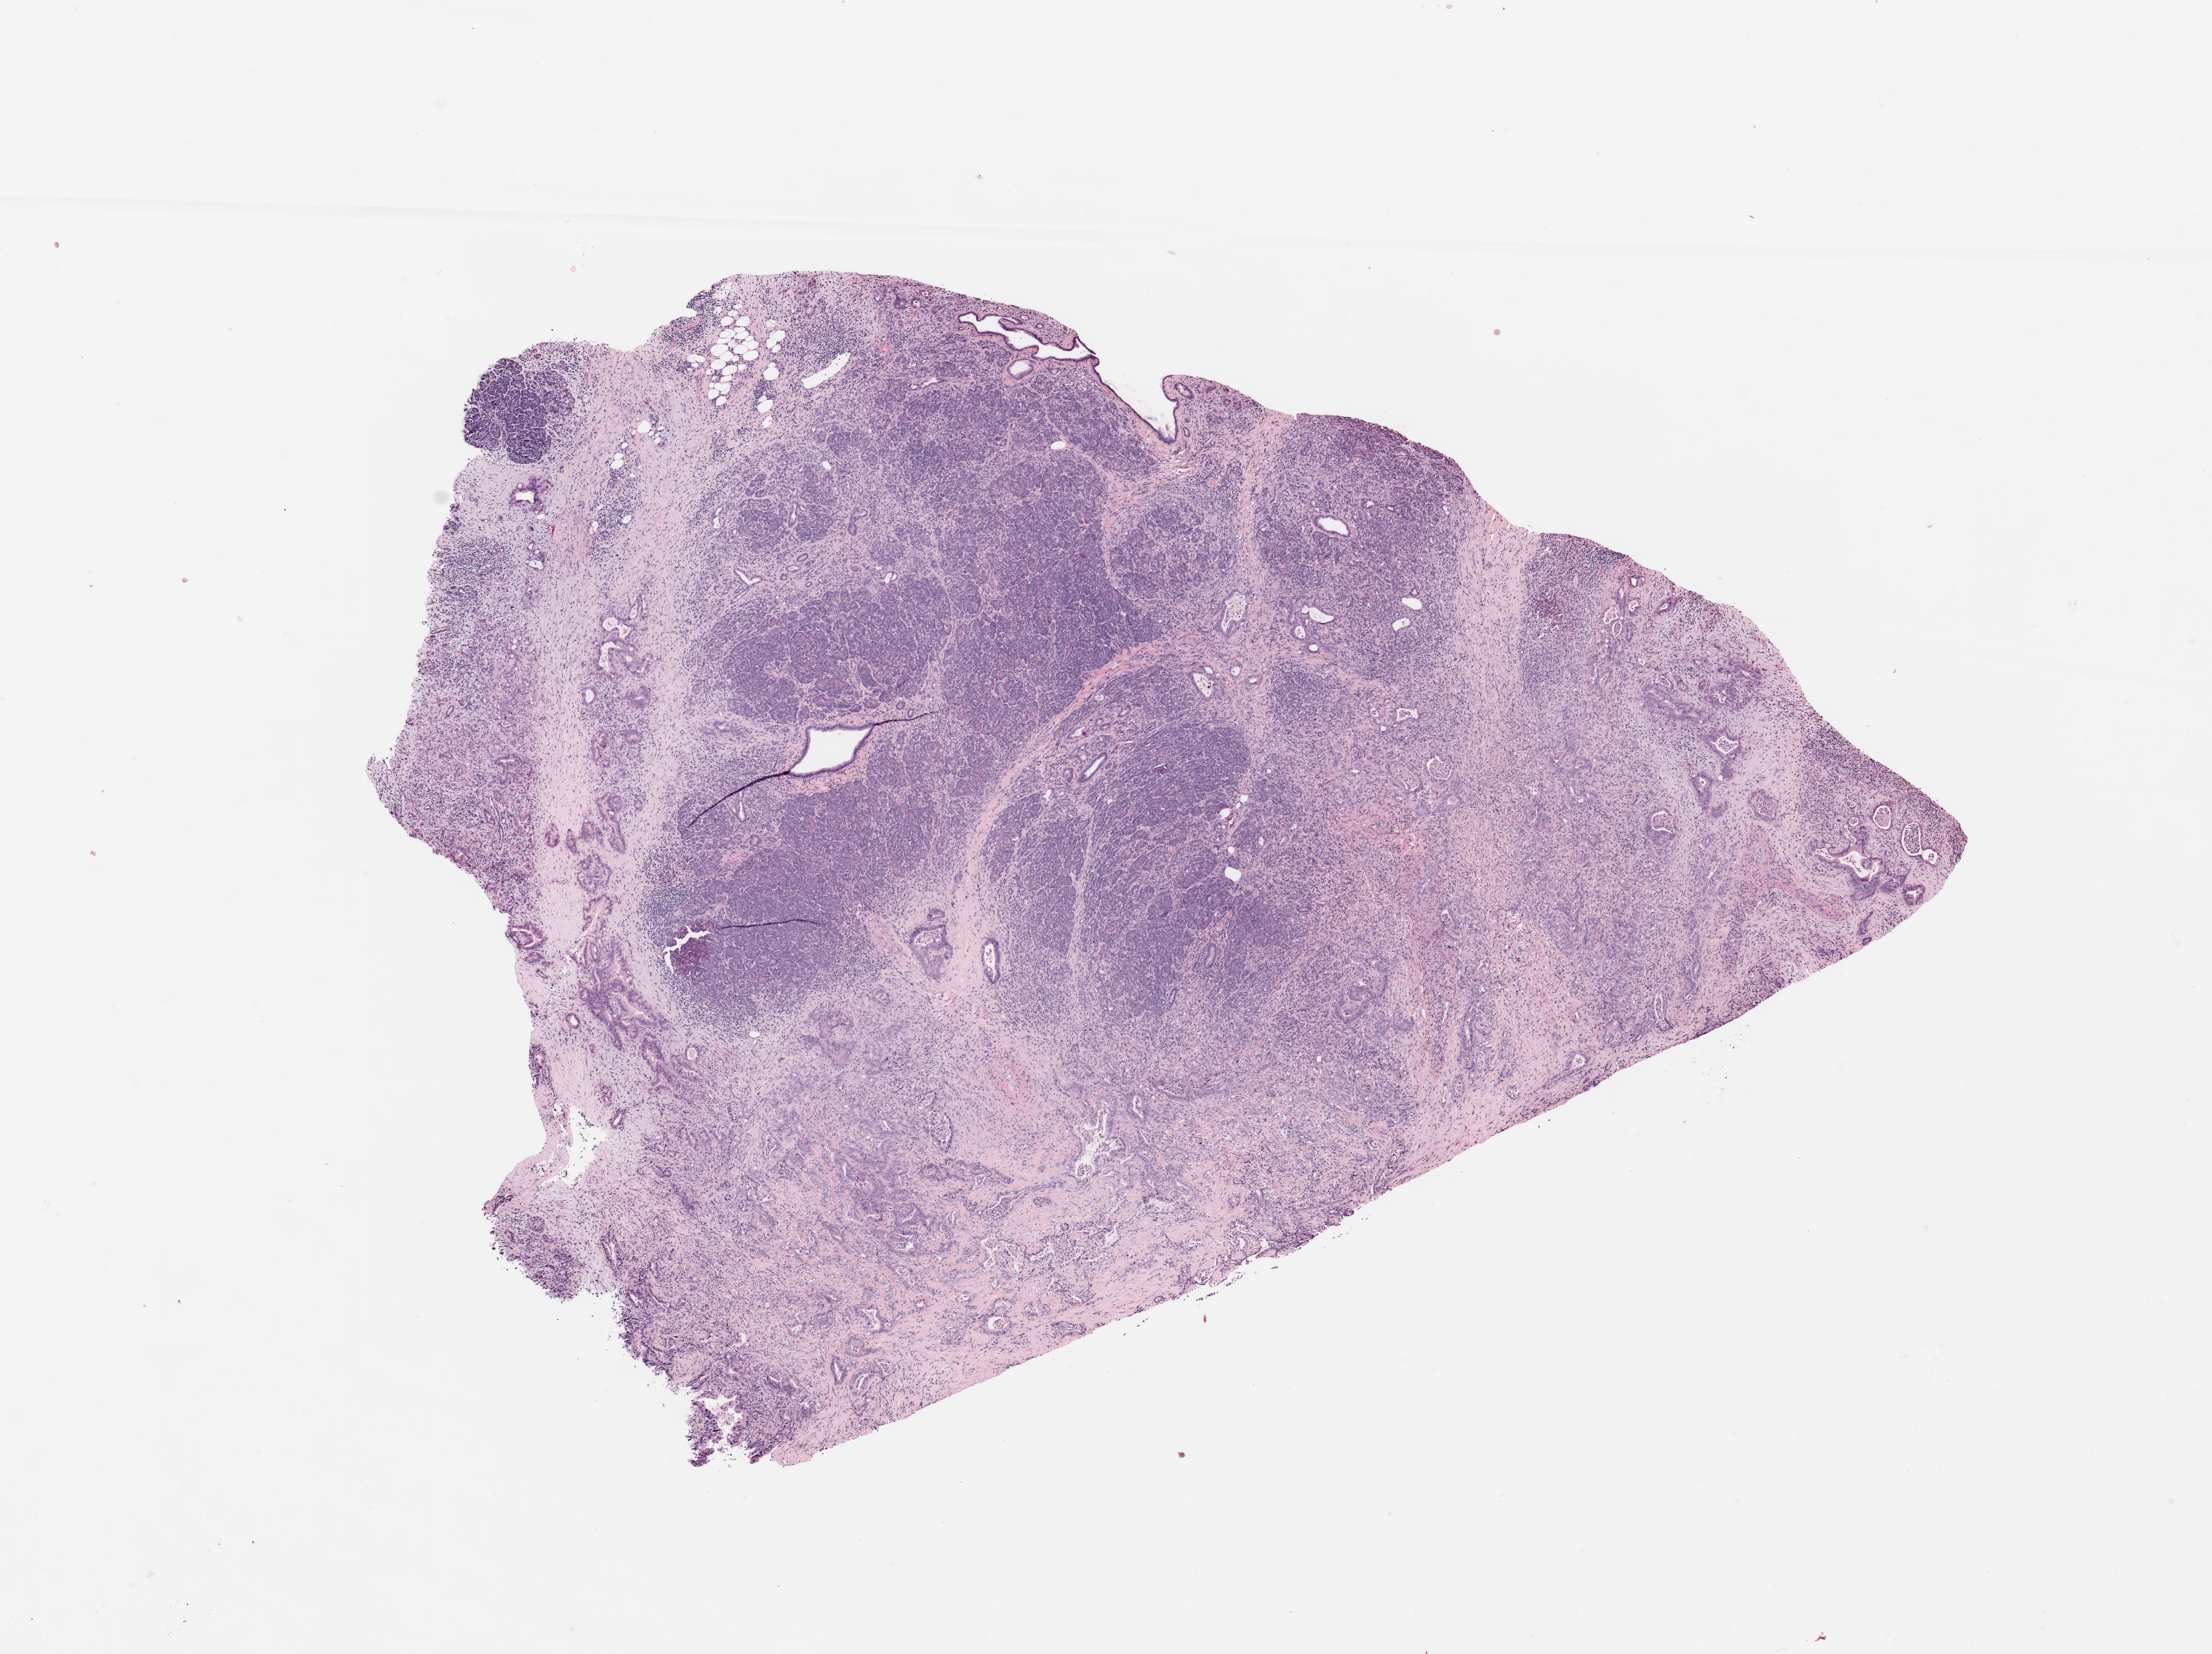
H&E whole-slide image, shown as a low-resolution overview of the whole scanned area (about 11.8 x 8.8 mm, from a 20x scan). Pancreas, tumour tissue. 73-year-old female patient. Histologic grade: G2 (moderately differentiated).
Diagnosis: Infiltrating duct carcinoma, NOS. Primary tumour site (as recorded): head.